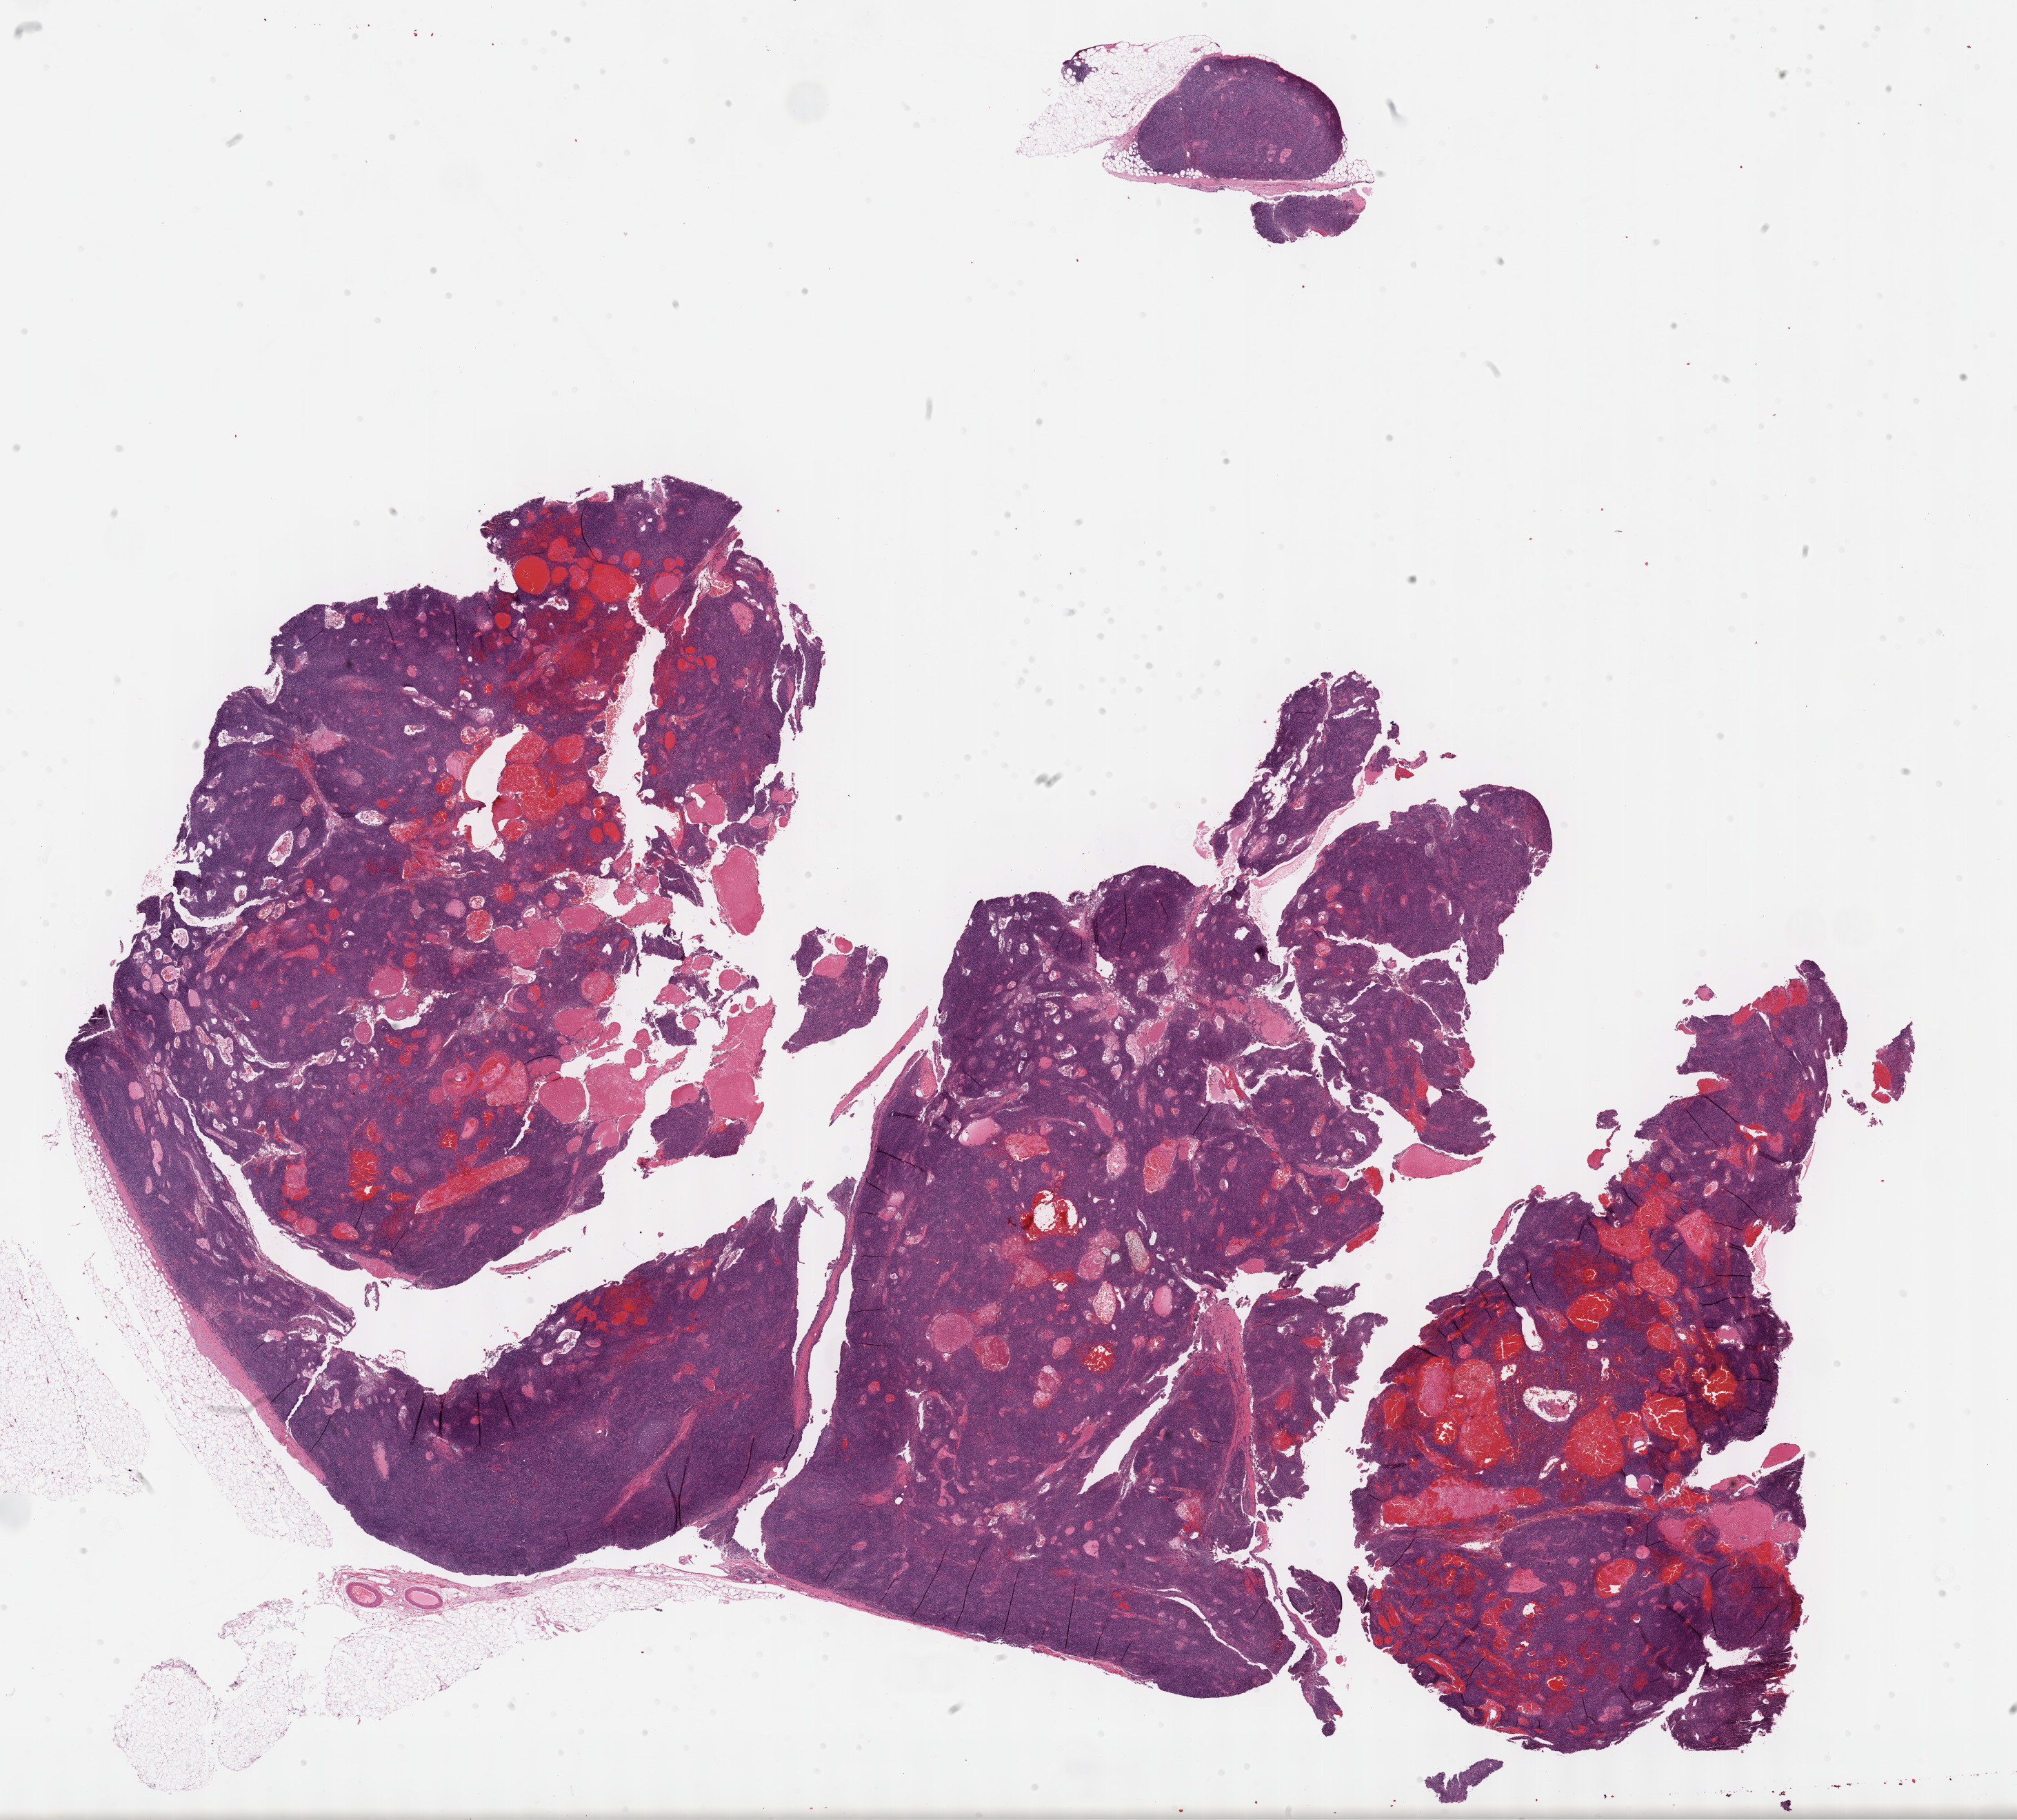
Digitized Hematoxylin and eosin (H&E) stained tissue section (whole slide), a low-resolution overview of the entire scanned area, about 23.7 x 21.3 mm. Formalin-fixed paraffin-embedded (FFPE) diagnostic section. Thymus, primary tumour sample. Female patient; age at initial diagnosis 69 years.
- histologic diagnosis: Thymoma, type B2, malignant